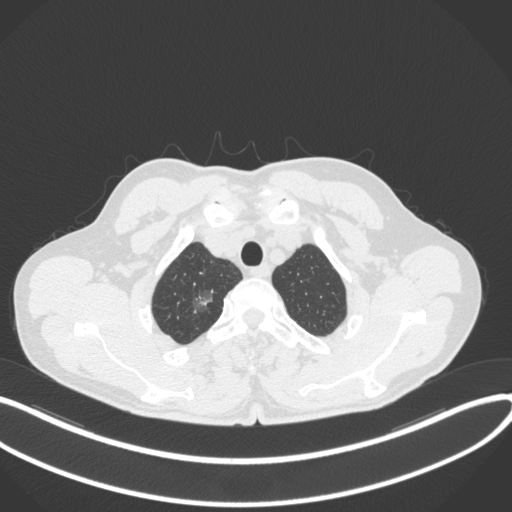
Chest CT, one axial slice; slice 340 of 407 in the series (ordered by position); reconstruction kernel B31f; 120 kVp; lung window (W 1500 / L -600 HU); 512 × 512 image matrix, field of view 400 × 400 mm. Patient: male, 58 years. Case-level facts recorded for this patient, not image findings: clinical TNM (as recorded): T1c N0 M0; histopathological grade: G1-2.
Annotated regions visible in this slice (rectangle marked by the reading radiologist):
- lung tumour (recorded histology: adenocarcinoma): bounding box [x1, y1, x2, y2] px = [187, 285, 215, 314]